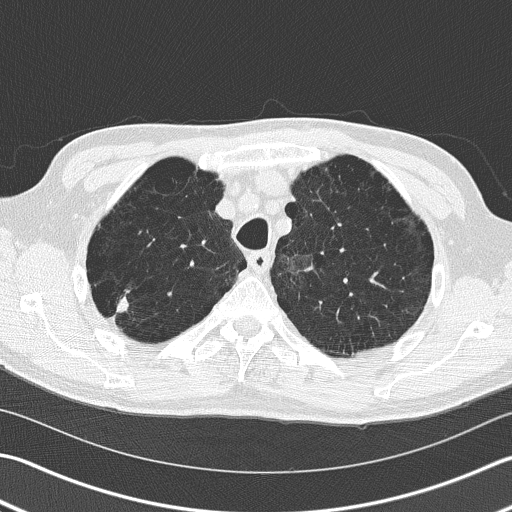
Chest CT (low-dose screening protocol), one axial image; first (baseline) screen; lung window (W 1500 / L -600 HU); 2 mm slice thickness. Male participant, aged 66 years at enrolment. Current smoker at enrolment.
Expert-annotated lung lesion, box from (x=93, y=277) to (x=148, y=339) px. Screening reader's record for this exam (one nodule recorded; not confirmed to be the boxed lesion): non-calcified nodule or mass ≥4 mm, right upper lobe, 39 × 23 mm, spiculated (stellate) margins, soft tissue attenuation. Lung cancer was diagnosed 36 days after this screen: squamous cell carcinoma, NOS, right upper lobe, poorly differentiated (G3), stage IB (AJCC 6th edition), 23 mm at pathology.